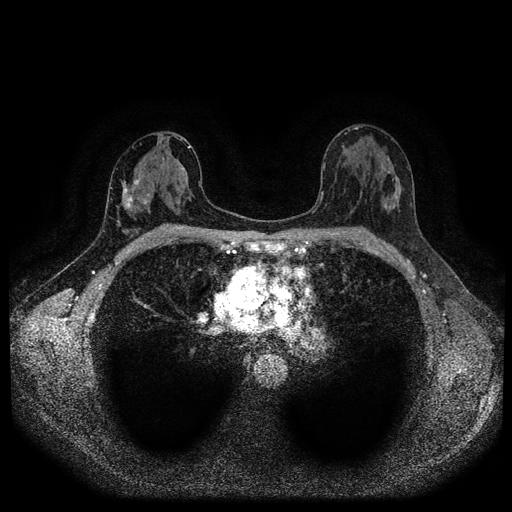
Breast MRI (dynamic contrast-enhanced, multi-phase), one axial slice. Slice 56 of 116 in the series (ordered by position). Dynamic contrast-enhanced series, time point 2 of 5 at this slice position (early post-contrast). 1.5 T. TE 2.7 ms, TR 5.4 ms. 512 × 512 image matrix, field of view 330 × 330 mm. Female patient, age 42 years.
Annotated regions visible in this slice (semi-automatically segmented with operator editing):
- breast lesion (labelled 'tumour' in the annotation; benign lesions carry a separate 'benign' label): bounding box <120,177,151,218> (left, top, right, bottom; pixels)